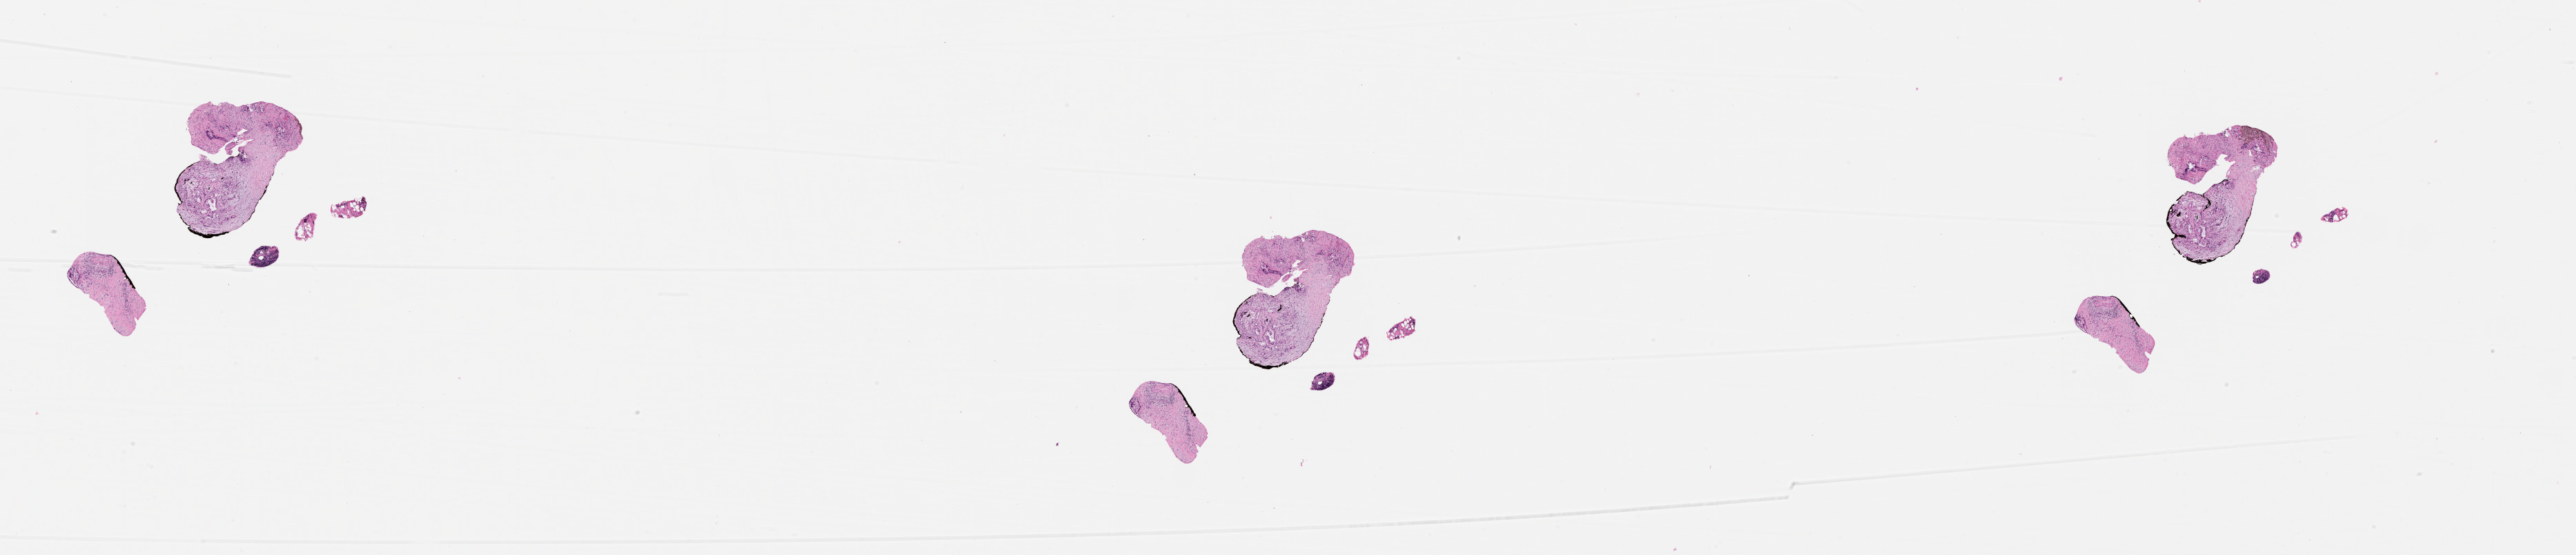
Whole-slide histology image, Hematoxylin and eosin (H&E) stained, shown as a low-resolution overview of the whole scanned area (about 30.1 x 6.5 mm), tumour tissue sample, sampled site: pancreas. 71-year-old female patient. Slide review estimates, as recorded: tumour nuclei 20%, necrosis 0%.
Diagnosis: Infiltrating duct carcinoma, NOS.